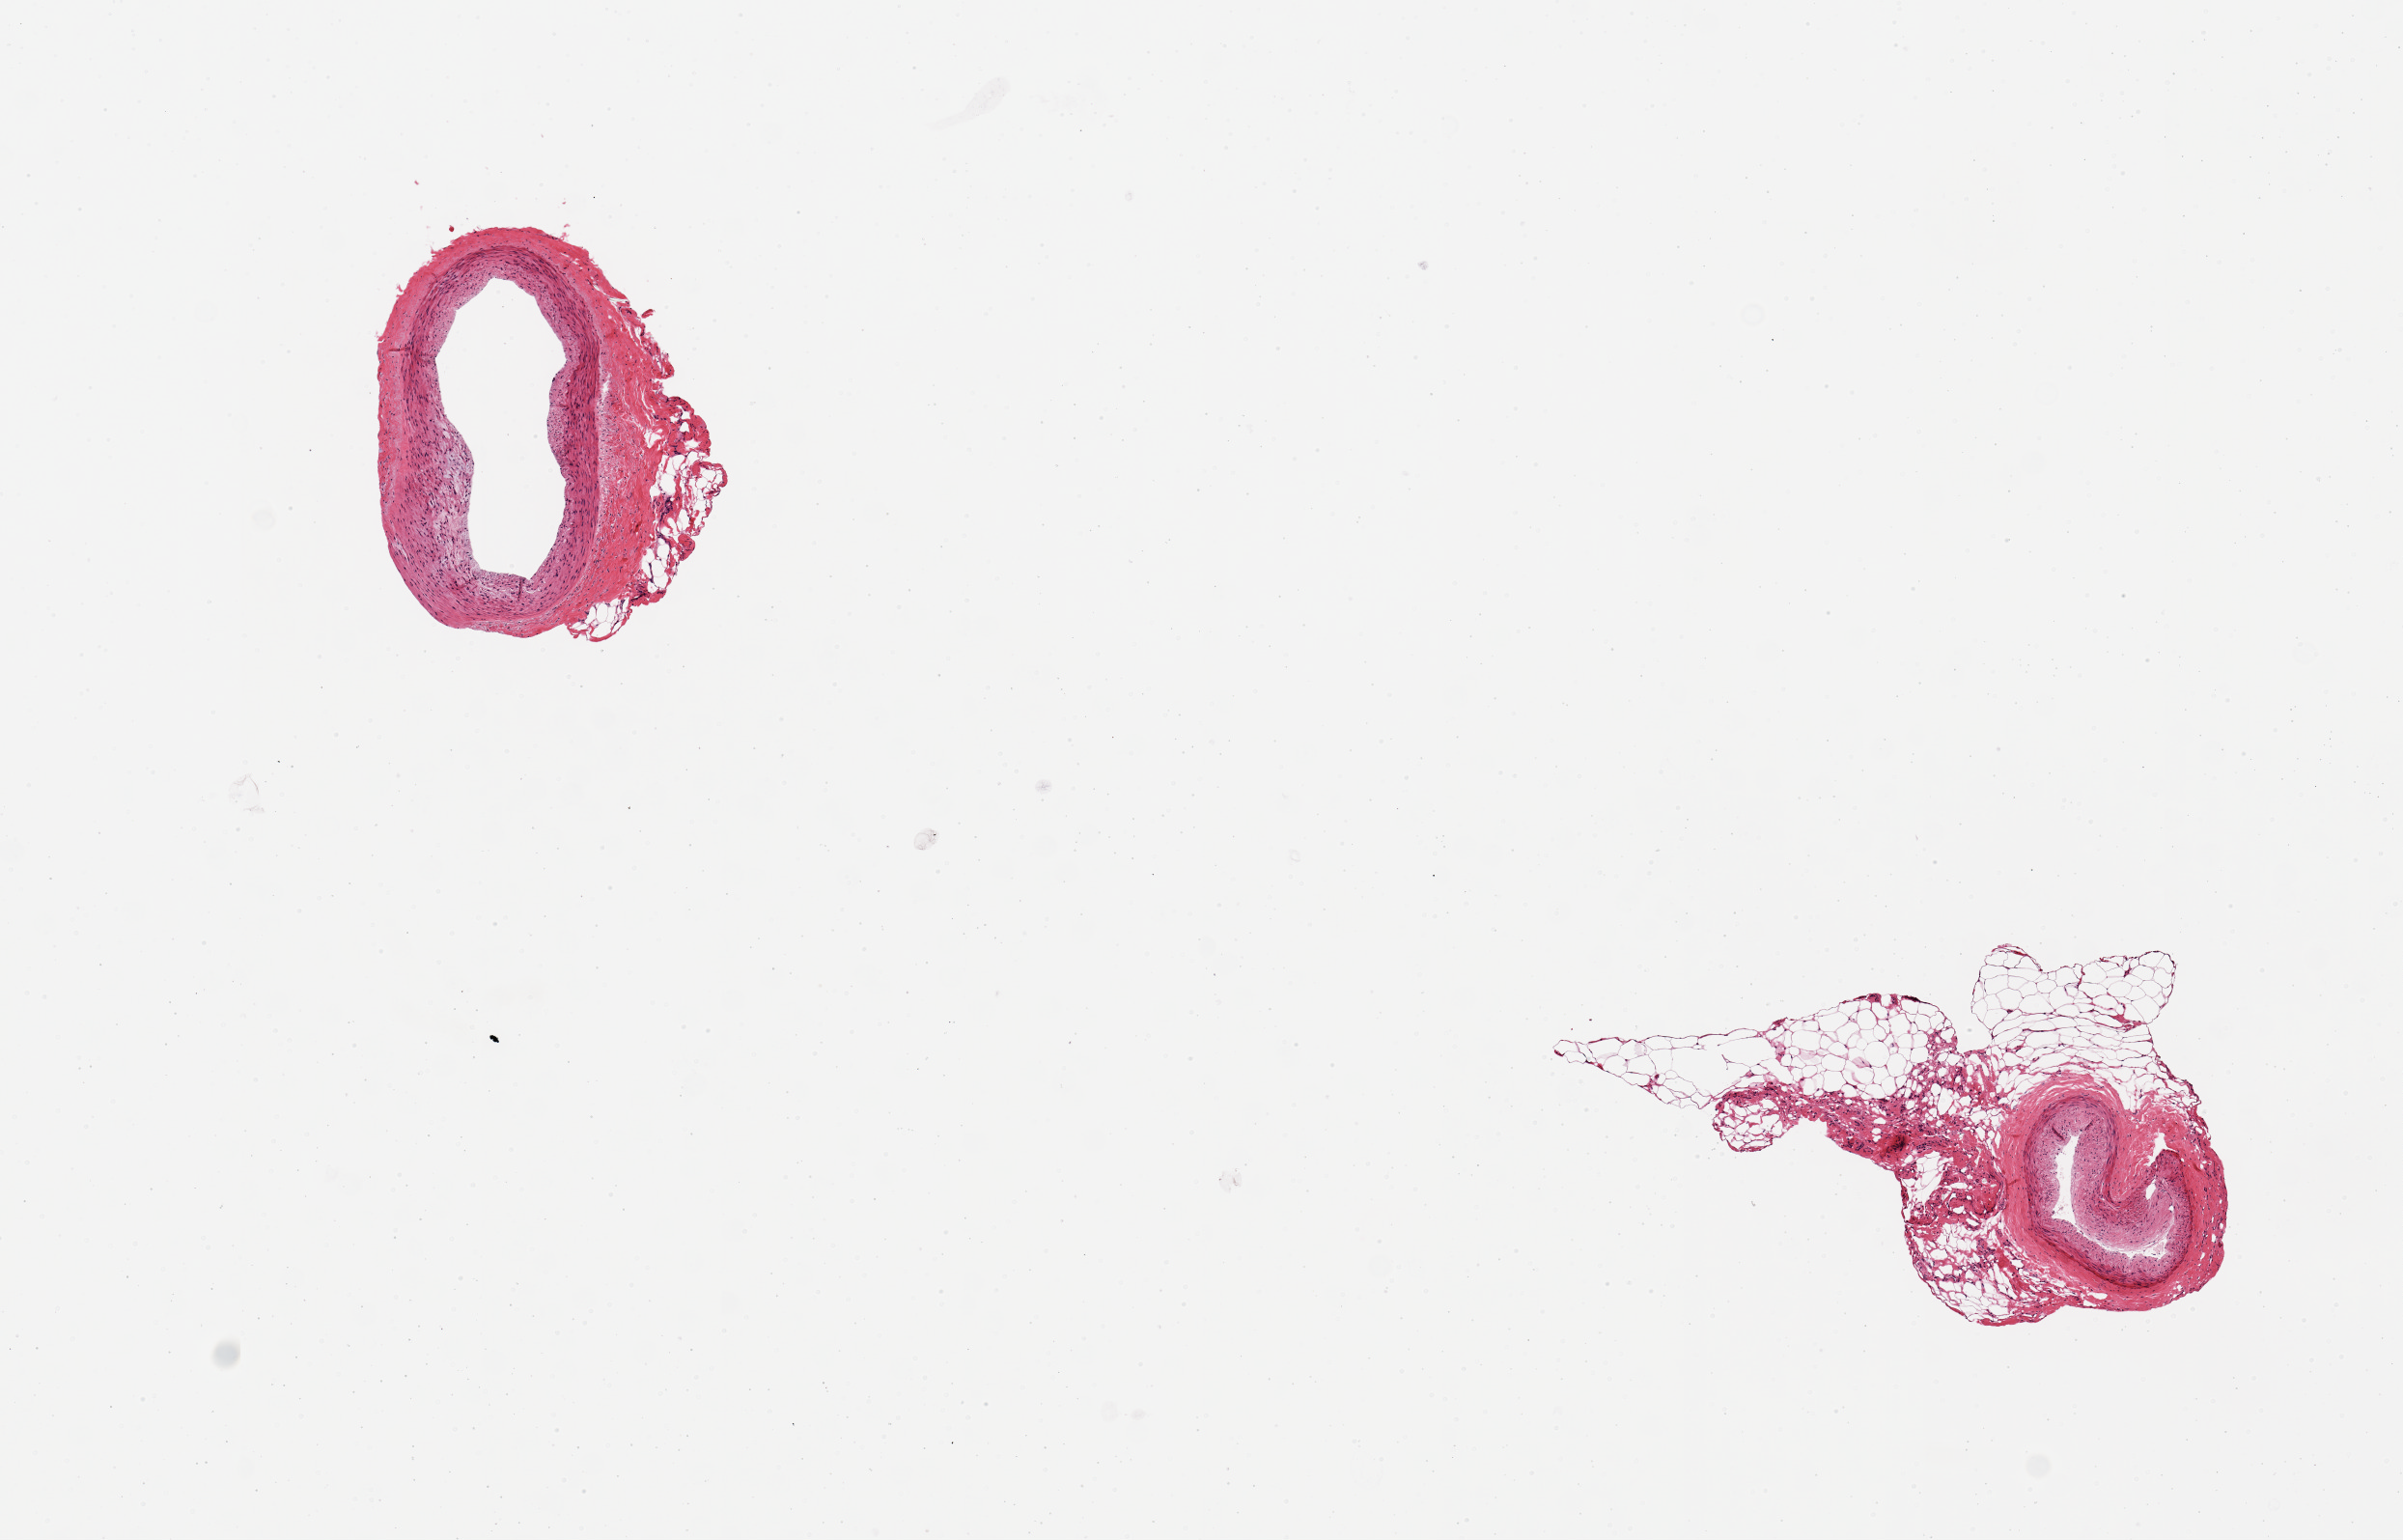
Whole-slide image, haematoxylin and eosin stain, brightfield — low-resolution overview of the scanned area, about 9.8 x 6.3 mm. PAXgene-fixed, paraffin-embedded tissue. Sampled site (target tissue): coronary artery. Tissue donor sample. Male donor.
Pathologist's review note for this sample: 2 pieces; intimal plaque mildly compromising lumen; 10 and 50% external fat.